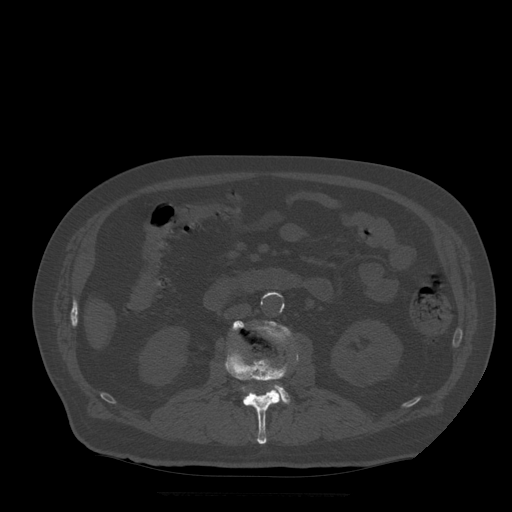
CT including the spine, one axial slice. Position 160 of 522 along the scan axis. Bone window (W 1800 / L 400 HU). 1.25 mm slice thickness. 512 × 512 image matrix, field of view 420 × 420 mm. Patient age 72 years. Case-level facts recorded for this patient, not image findings: primary cancer: prostate.
Annotated regions visible in this slice (semi-automatically segmented with operator editing):
- L2 vertebra: bounding box (x1, y1, x2, y2) in pixels: (225, 348, 299, 444)
- L3 vertebra: (233, 321, 291, 403)